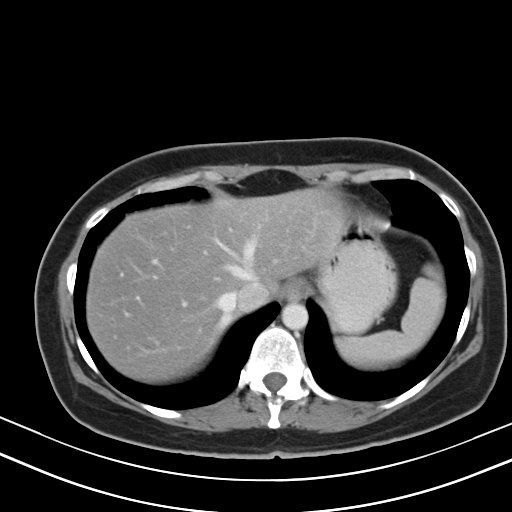
Contrast-enhanced abdominal CT, one axial slice; position 40 of 47 along the scan axis; reconstruction kernel B40s; intravenous contrast given; soft-tissue window (W 400 / L 40 HU); 5 mm slice thickness; 512 × 512 image matrix. Female patient. From the clinical record (not read from this slice): diagnosis: colorectal cancer liver metastases, imaged before liver resection; multiple liver metastases: no; largest metastasis: 3.5 cm; disease in both lobes: no.
Structures marked on this image (manually delineated by an expert):
- hepatic veins: bounding box [x1, y1, x2, y2] px = [125, 225, 262, 324]
- liver: [88, 195, 336, 380]
- planned liver remnant (the part of the liver to remain after resection): [88, 195, 336, 380]
- portal vein (with intrahepatic branches): [140, 336, 162, 356]